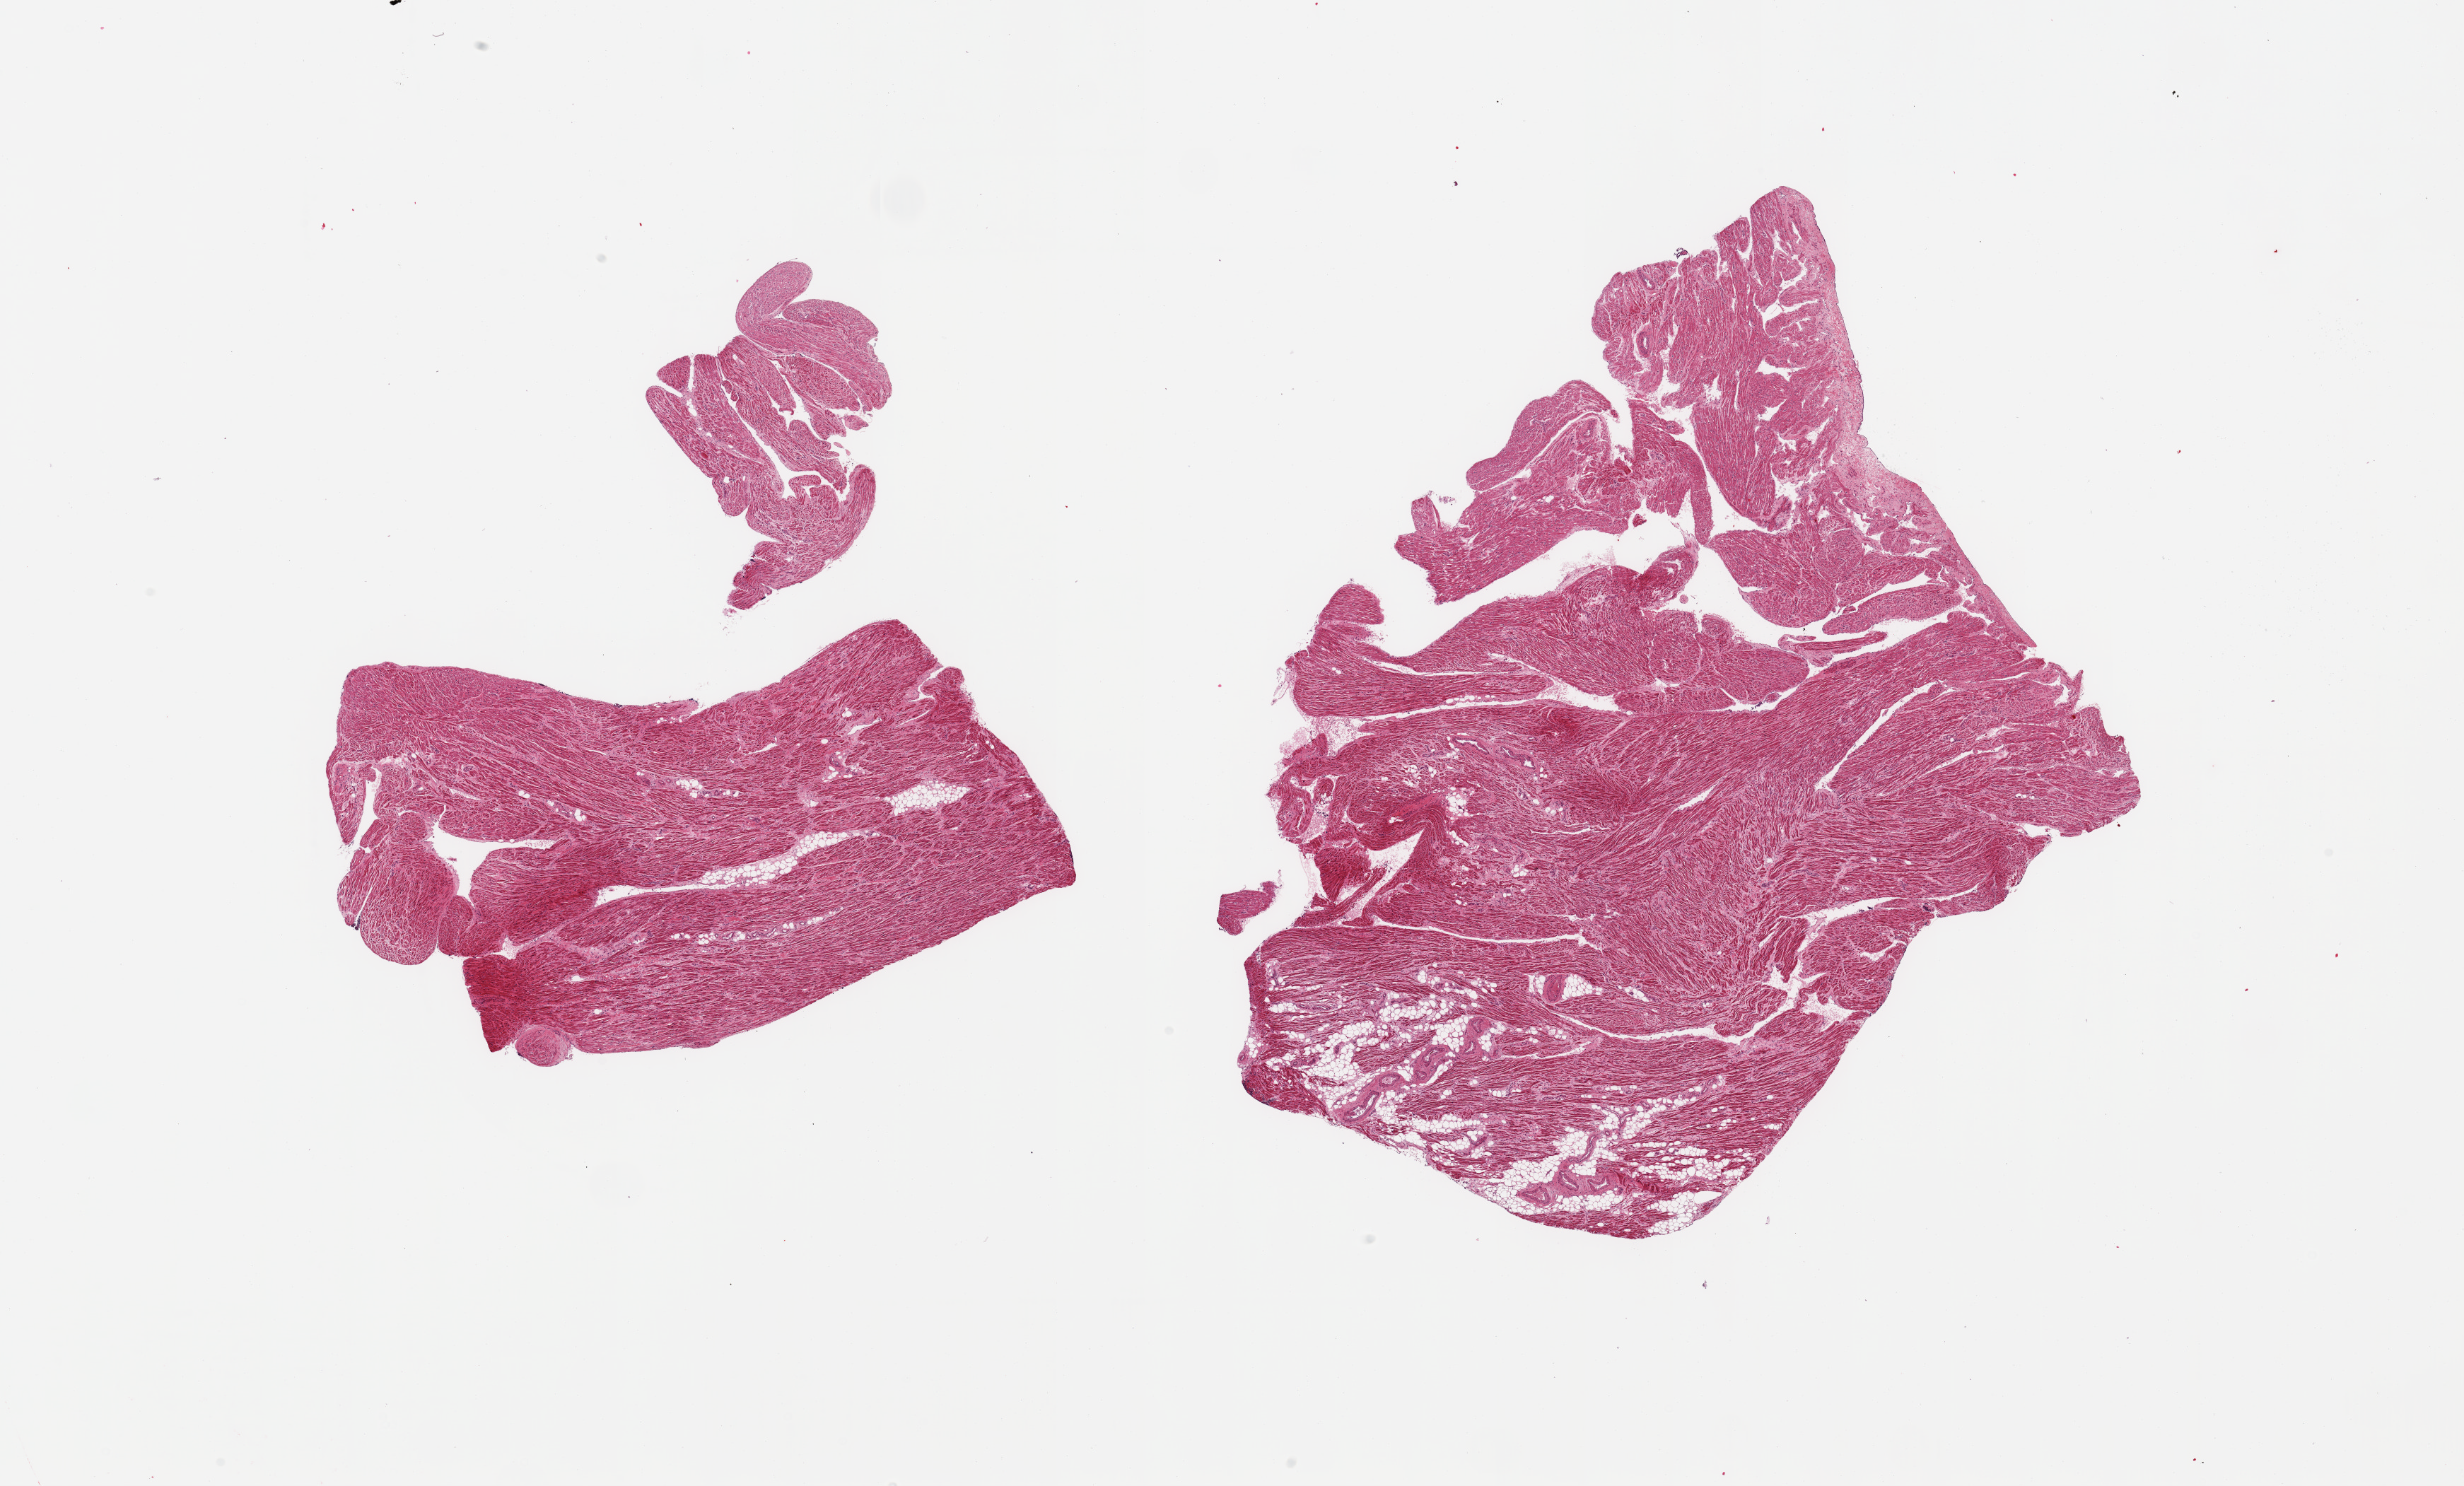
Whole-slide image, haematoxylin and eosin stain, a low-resolution overview of the entire scanned area, about 27.6 x 16.6 mm; PAXgene-fixed, paraffin-embedded tissue; target tissue: auricular appendage; donor tissue sample. Donor sex: male.
• reviewer comment on this tissue sample: 2 pieces; 5% & 10% internal fat